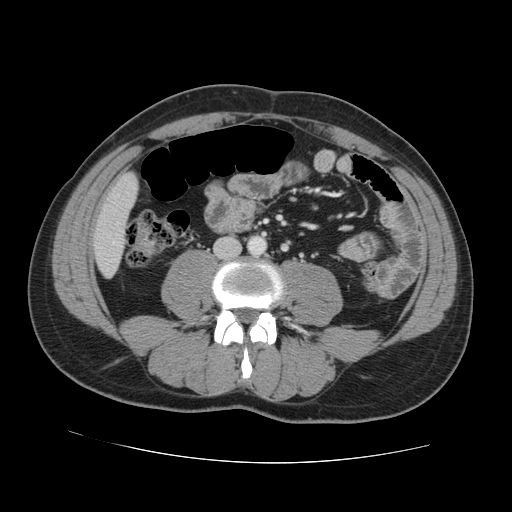
Contrast-enhanced abdominal CT, one axial slice; position 18 of 131 along the scan axis; 120 kVp; intravenous contrast given; soft-tissue window (W 400 / L 40 HU); 2.5 mm slice thickness; 512 × 512 image matrix, field of view 380 × 380 mm. Male patient, age 40 years. Case-level facts recorded for this patient, not image findings: diagnosis: colorectal cancer liver metastases, imaged before liver resection; multiple liver metastases: yes; largest metastasis: 2.9 cm; disease in both lobes: yes.
Outlined on this slice (expert manual segmentation):
- liver: box from (x=95, y=175) to (x=137, y=275) px